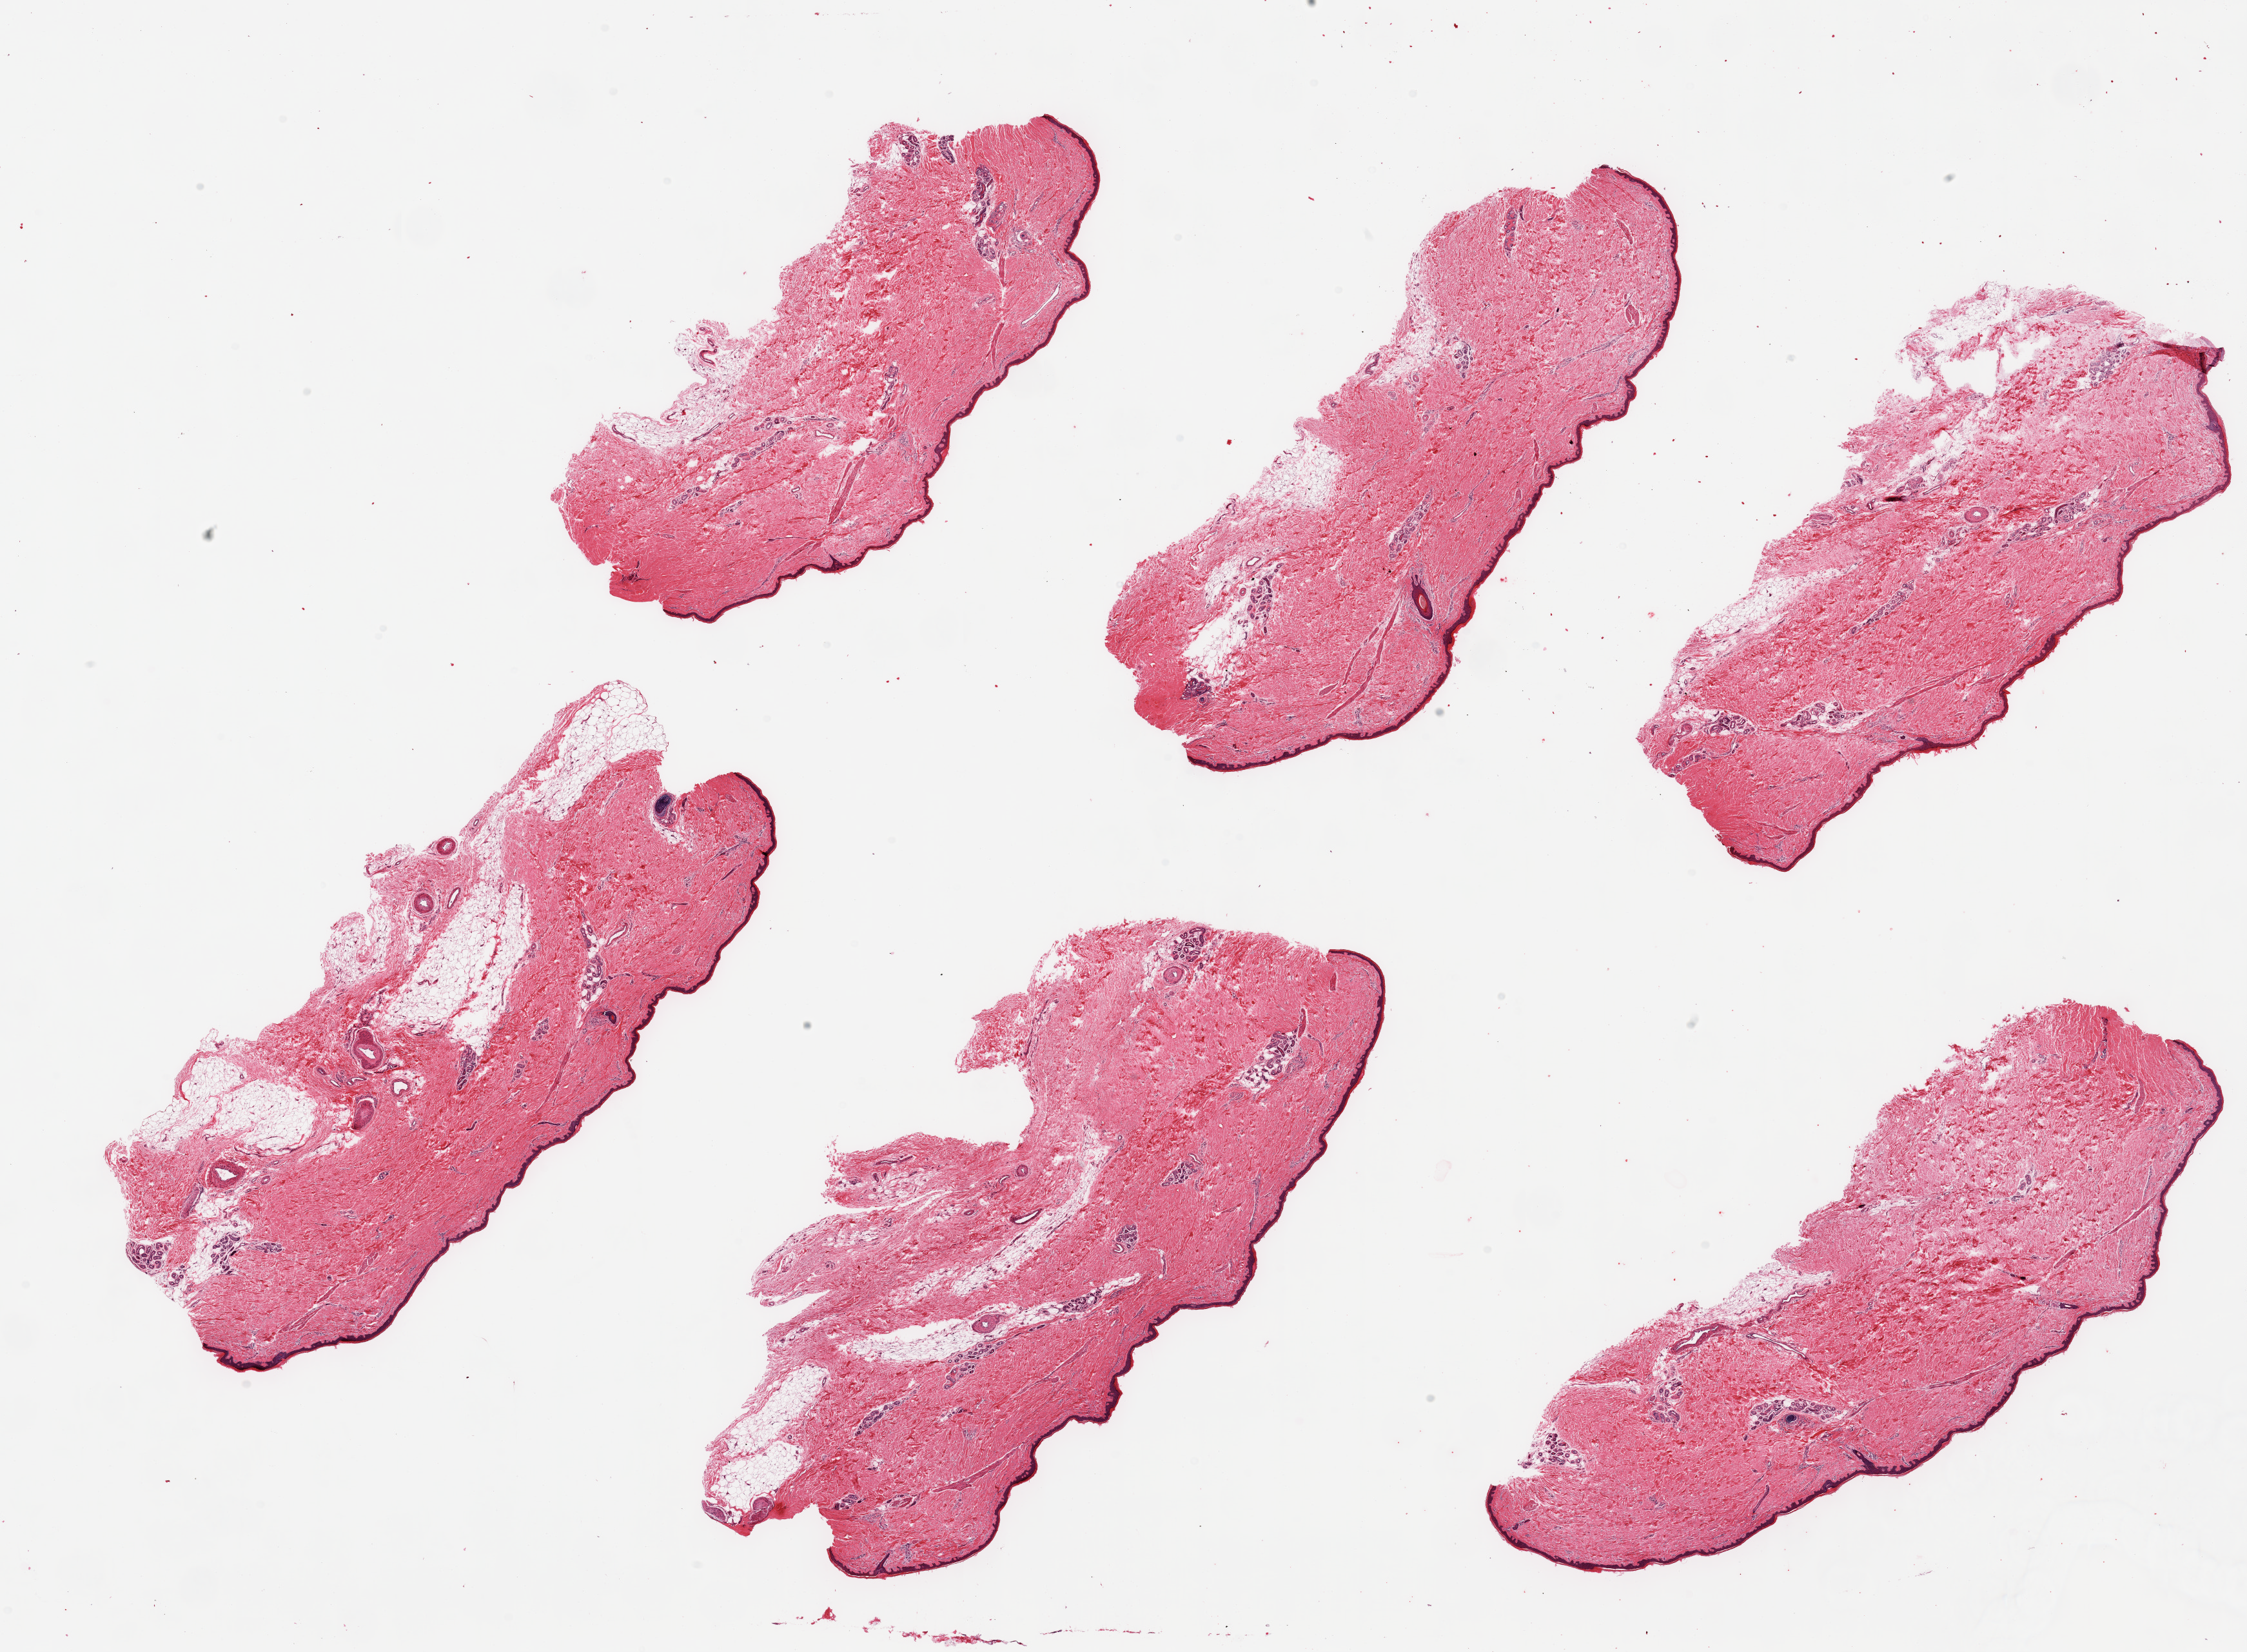
Whole-slide image, hematoxylin and eosin (H&E) stain — a low-resolution overview of the entire scanned area, about 27.6 x 20.3 mm, PAXgene-fixed paraffin-embedded (PFPE) section, sampled site (target tissue): skin of lower leg, tissue donor sample. Donor sex: male.
* pathologist's review note for this sample: 6 pieces; includes 5-20% internal/external fat, epidermis measures 47 microns